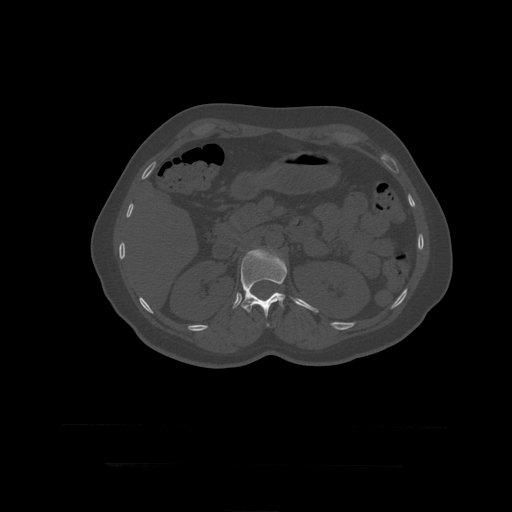
CT including the spine, one axial slice. Slice 172 of 399 in the series (ordered by position). 120 kVp. Bone window (W 1800 / L 400 HU). 512 × 512 image matrix, field of view 450 × 450 mm. Patient age 41 years. Case-level facts recorded for this patient, not image findings: primary cancer: breast.
Structures marked on this image (semi-automatically segmented with operator editing):
- L1 vertebra: box from (x=241, y=249) to (x=288, y=327) px